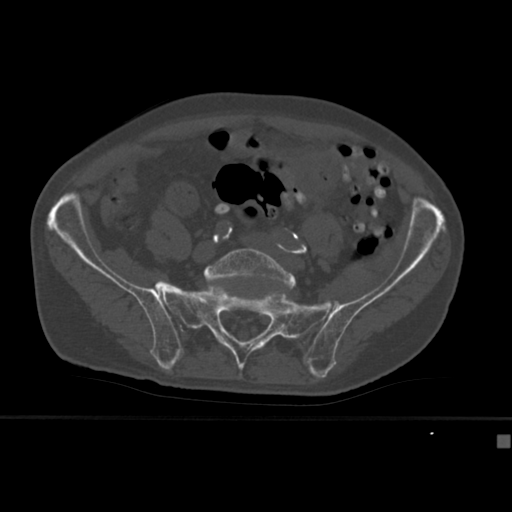
CT including the spine, one axial slice; slice 74 of 430 in the series (ordered by position); reconstruction kernel Br40s; 120 kVp; bone window (W 1800 / L 400 HU); 512 × 512 image matrix, field of view 337 × 337 mm. Male patient, age 64 years. Case-level facts recorded for this patient, not image findings: primary cancer: uterus; vertebrae with lytic lesions (as recorded): T1, T4, T5, T7, L5.
Outlined on this slice (semi-automatic segmentation, software-assisted and operator-edited):
- L5 vertebra: bounding box <204,248,296,290> (left, top, right, bottom; pixels)